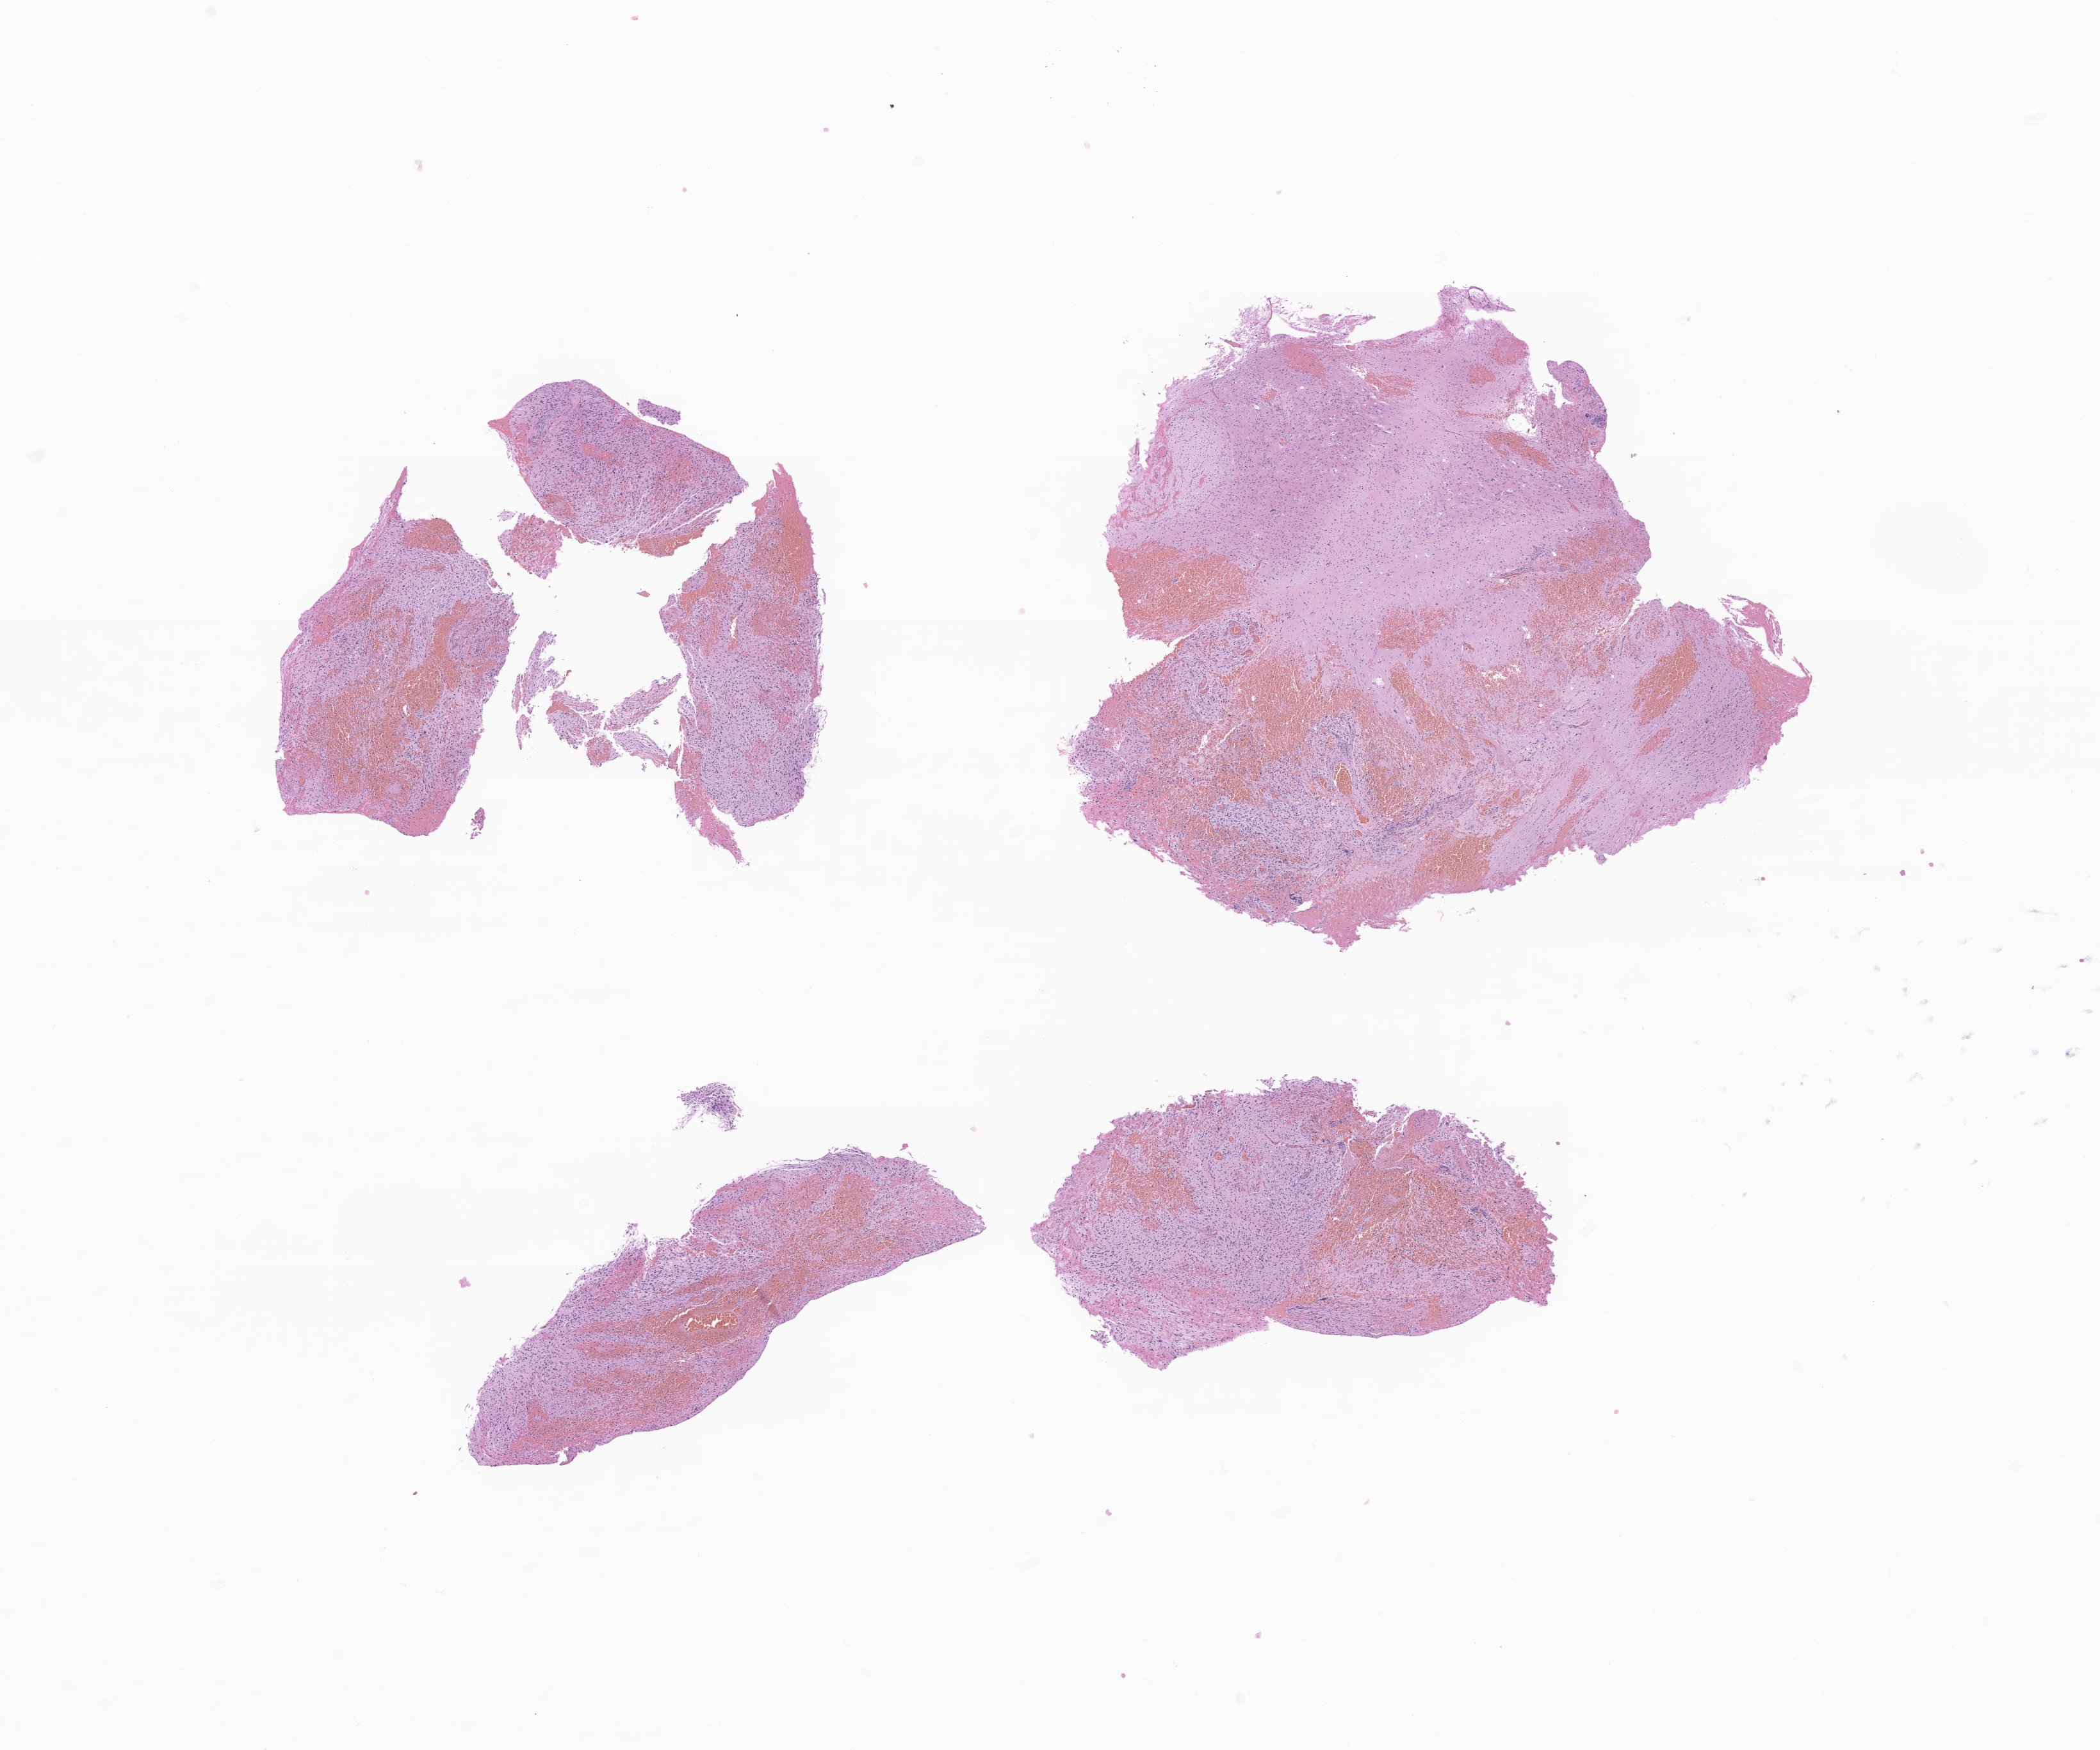
H&E whole-slide image of tumor tissue from the spinal cord — low-resolution overview of the scanned area, about 13.8 x 11.5 mm, formalin-fixed, paraffin-embedded (FFPE) tissue. Patient: female, age 180 months.
Diagnosis: Glioma, malignant.